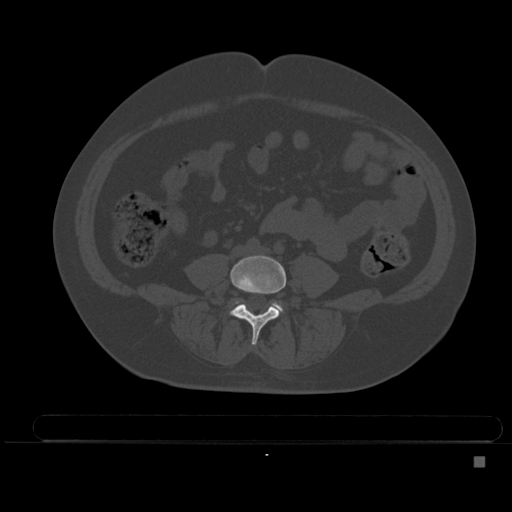
CT including the spine, one axial slice. Slice 124 of 495 in the series (ordered by position). Bone window (W 1800 / L 400 HU). 512 × 512 image matrix, field of view 404 × 404 mm. Patient: female, 33 years. From the clinical record (not read from this slice): primary cancer: breast; vertebrae with lytic lesions (as recorded): T1.
Annotated regions visible in this slice (semi-automatically segmented with operator editing):
- L4 vertebra: box from (x=231, y=255) to (x=286, y=345) px
- L5 vertebra: (x=273, y=303)–(x=281, y=310)